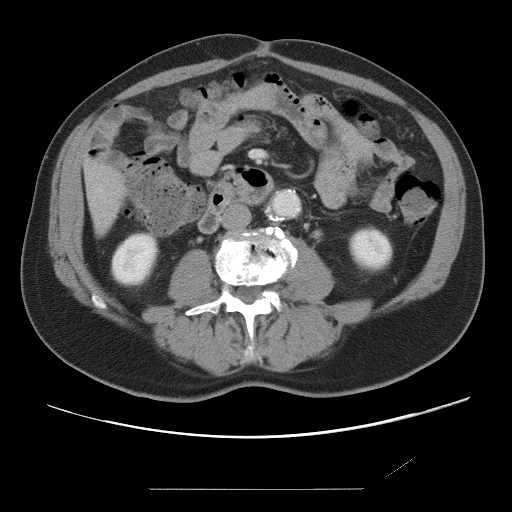
Contrast-enhanced abdominal CT, one axial slice. Position 11 of 87 along the scan axis. Intravenous contrast given. Soft-tissue window (W 400 / L 40 HU). 5 mm slice thickness. 512 × 512 image matrix. Male patient, age 74 years. From the clinical record (not read from this slice): diagnosis: colorectal cancer liver metastases, imaged before liver resection; multiple liver metastases: yes; largest metastasis: 1.1 cm; chemotherapy before resection: yes.
Annotated regions visible in this slice (outlined manually by an expert reader):
- liver: bounding box (x1, y1, x2, y2) in pixels: (85, 160, 121, 230)
- planned liver remnant (the part of the liver to remain after resection): (85, 161, 121, 230)